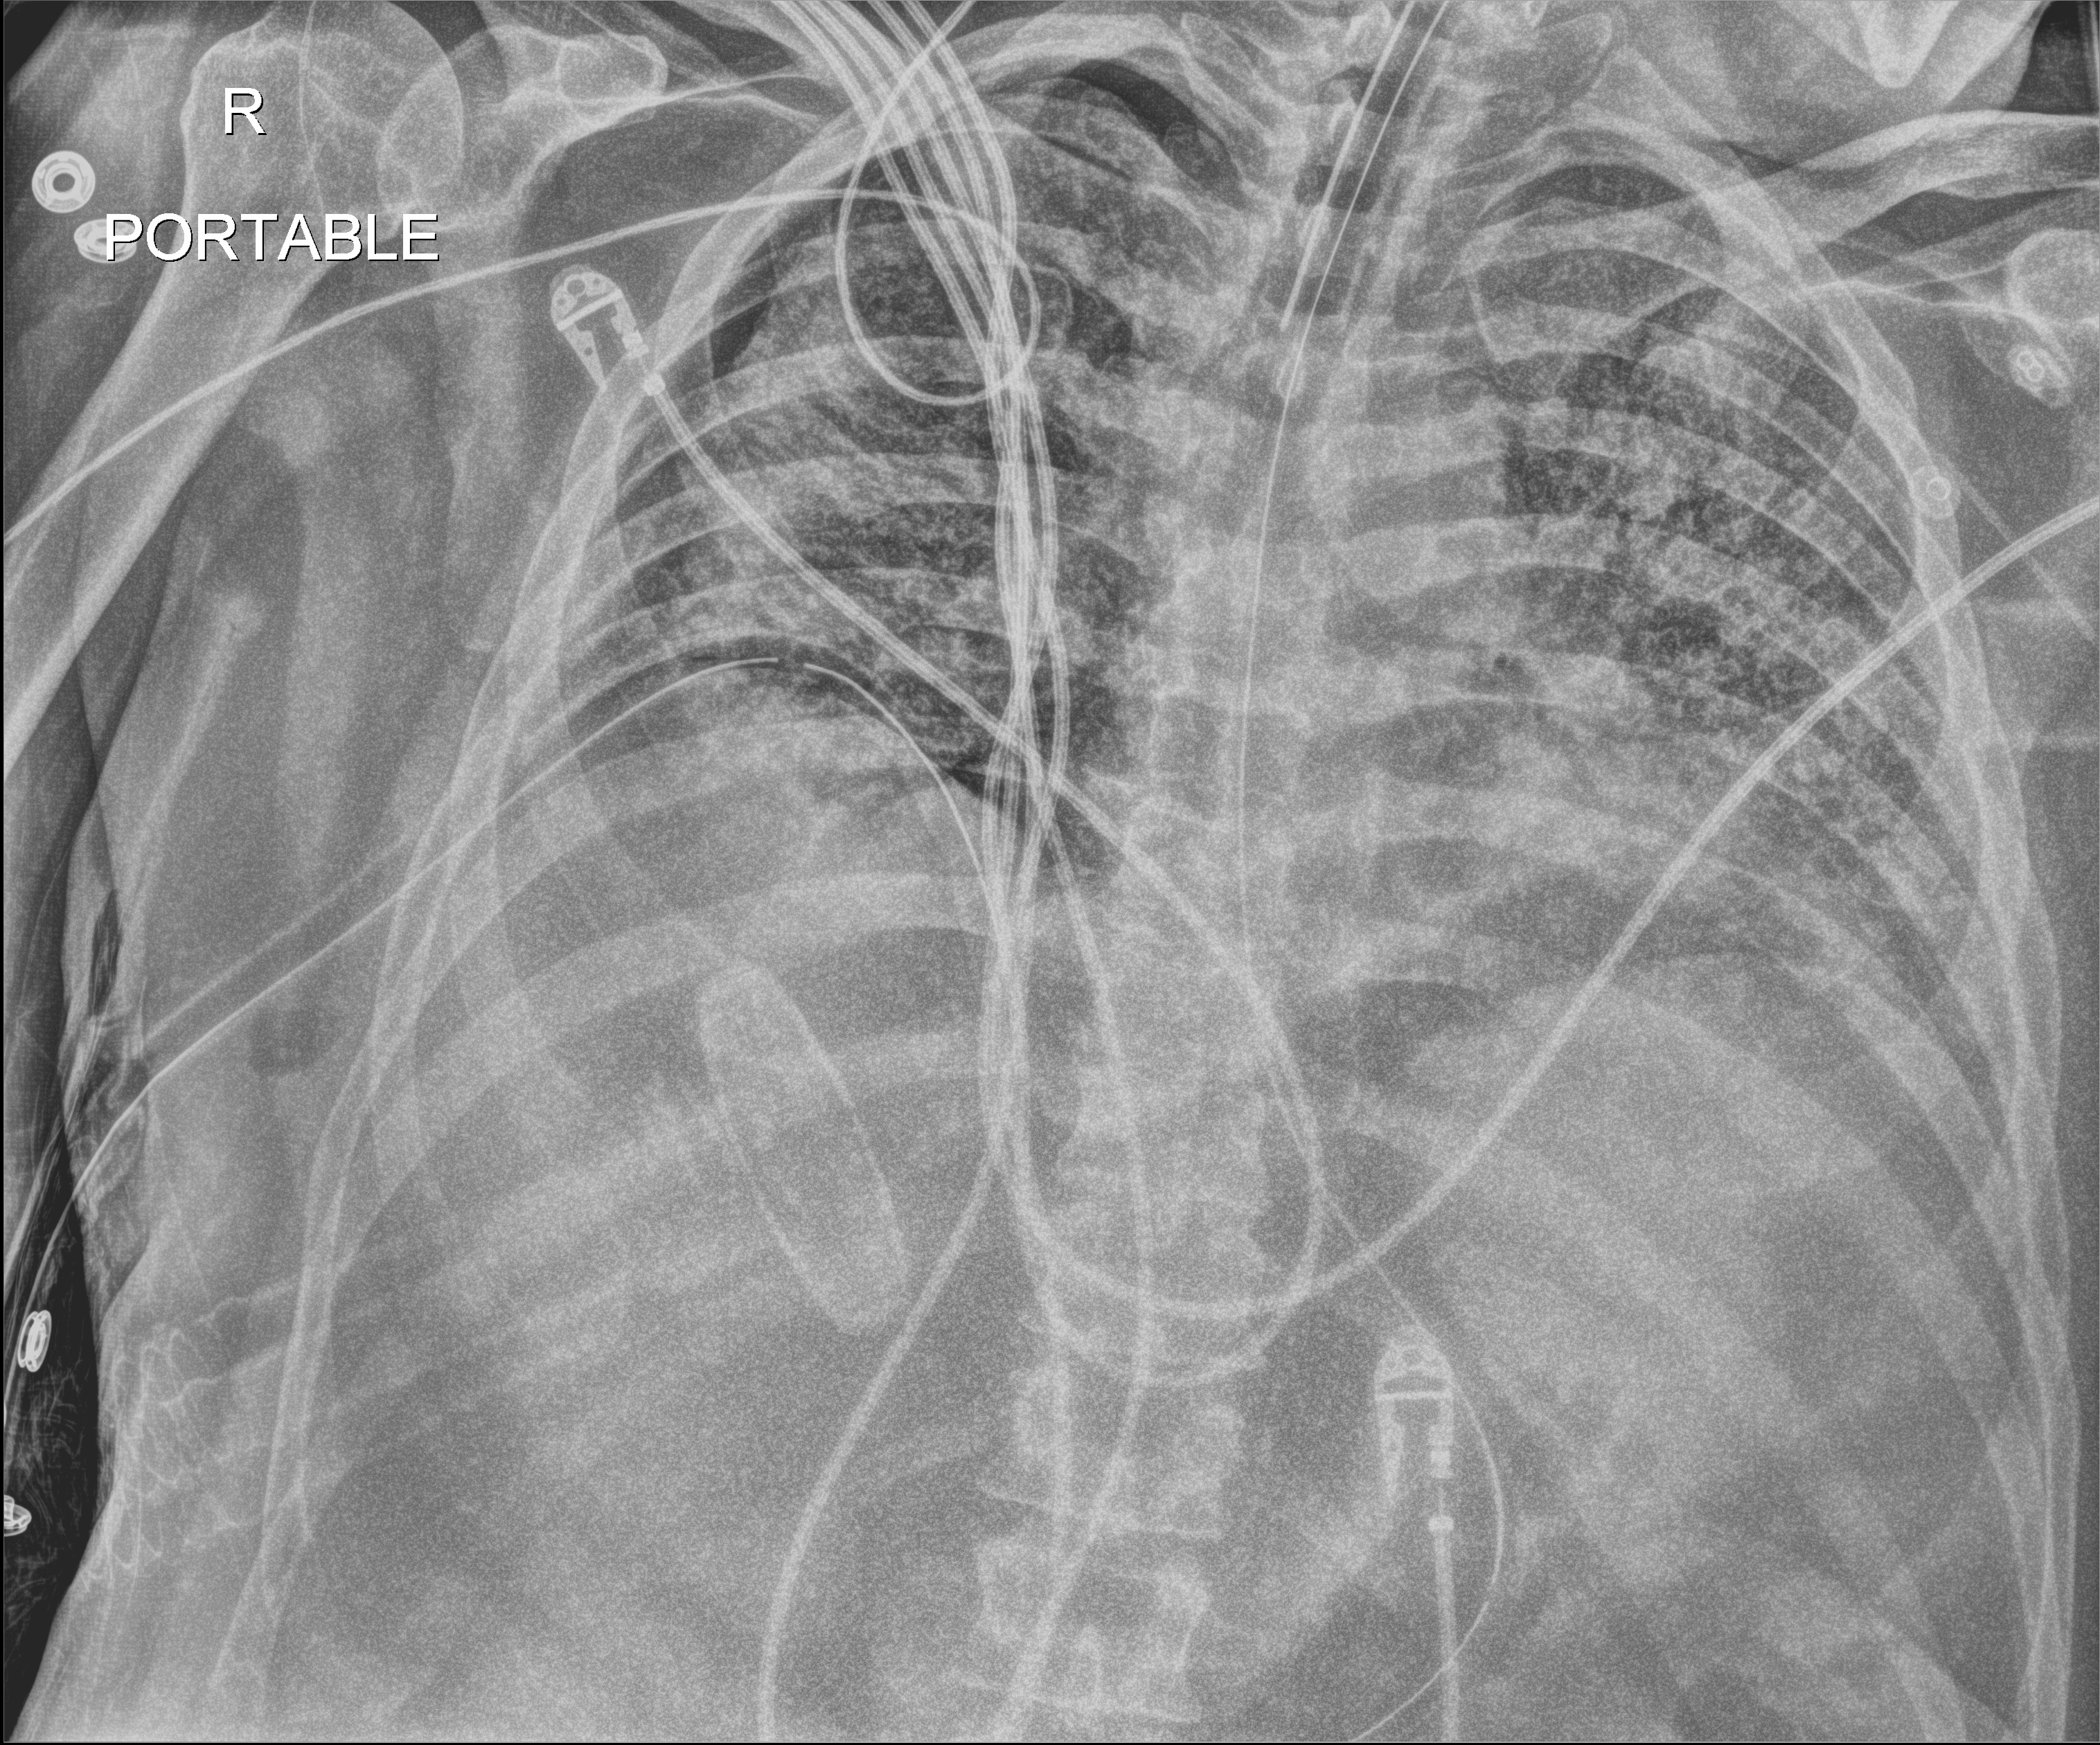
Portable chest radiograph, anteroposterior (AP) projection. Male patient hospitalised with COVID-19, age 18–59 years.
From the hospital-stay record, not from the radiograph (when in the stay this image was taken is not recorded): chronic kidney disease (admission record): no; hypertension (admission record): yes.